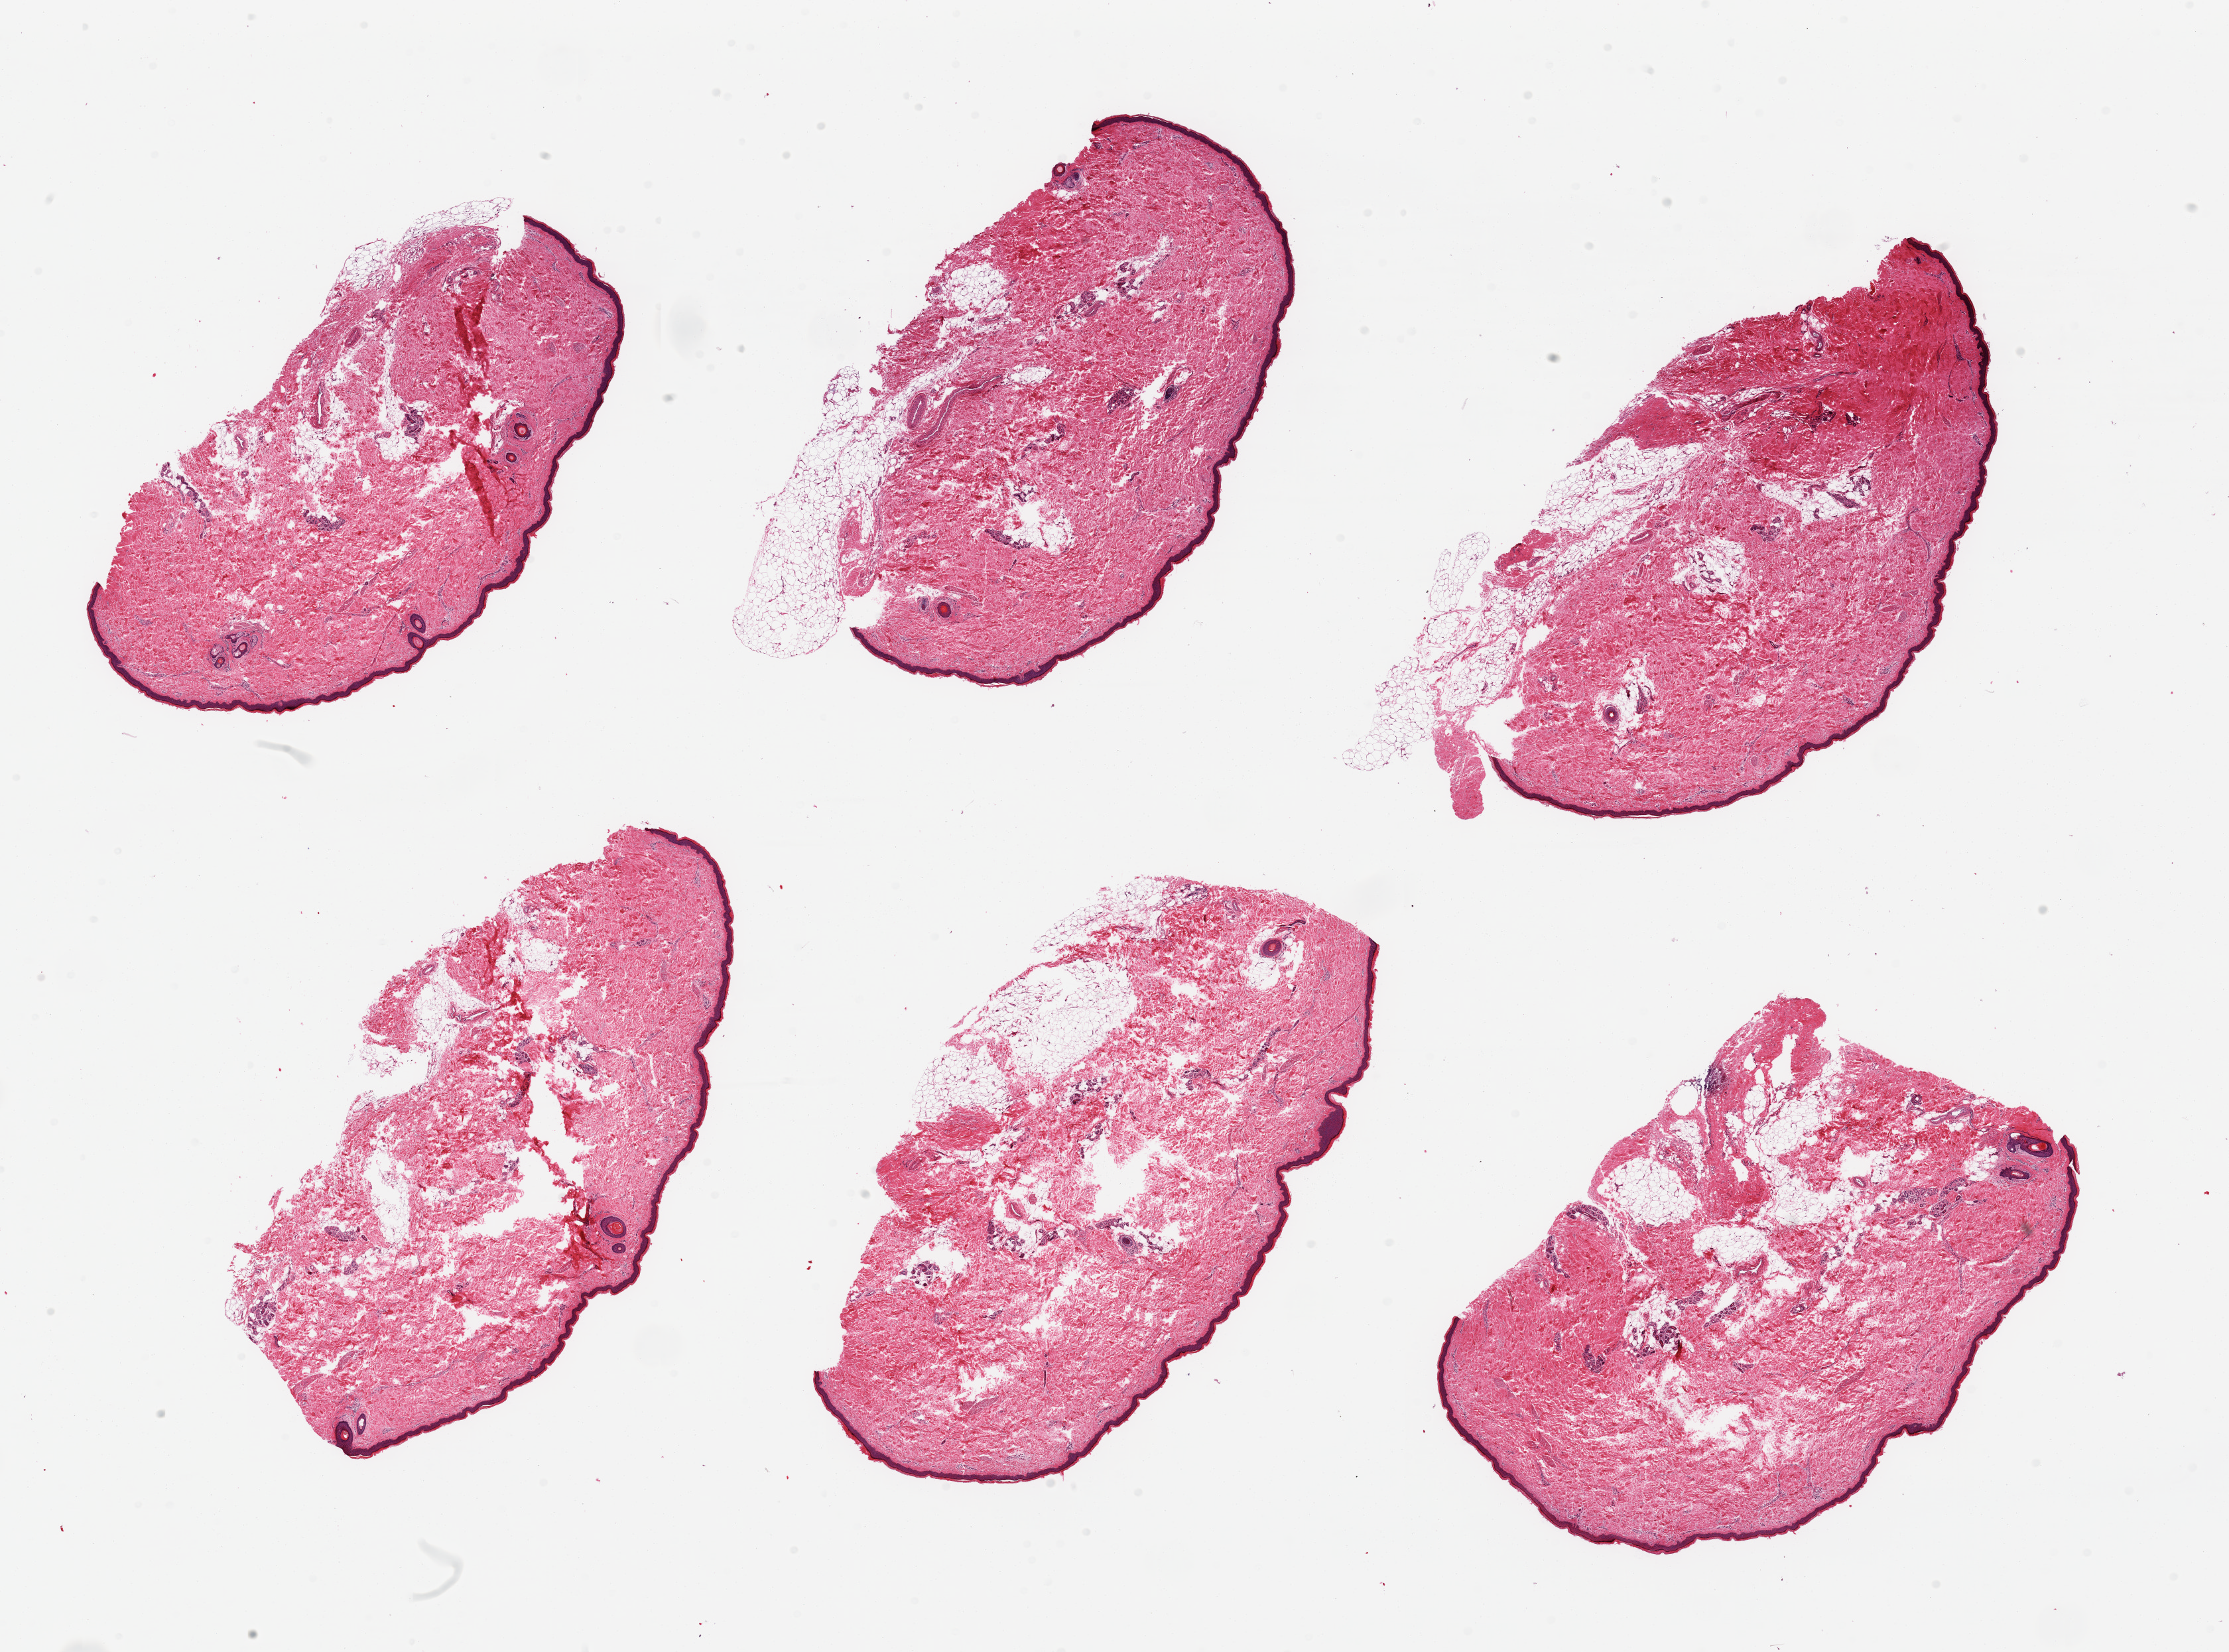
Digitized haematoxylin and eosin-stained section — a low-resolution overview of the entire scanned area, about 26.6 x 19.7 mm, PAXgene-fixed paraffin-embedded (PFPE) section, target tissue: skin of lower leg, tissue donor sample. Donor: male.
- review note (as recorded): 6 pieces, adherent/dermal fat, moderate, squamous epithelium is ~50-6- microns